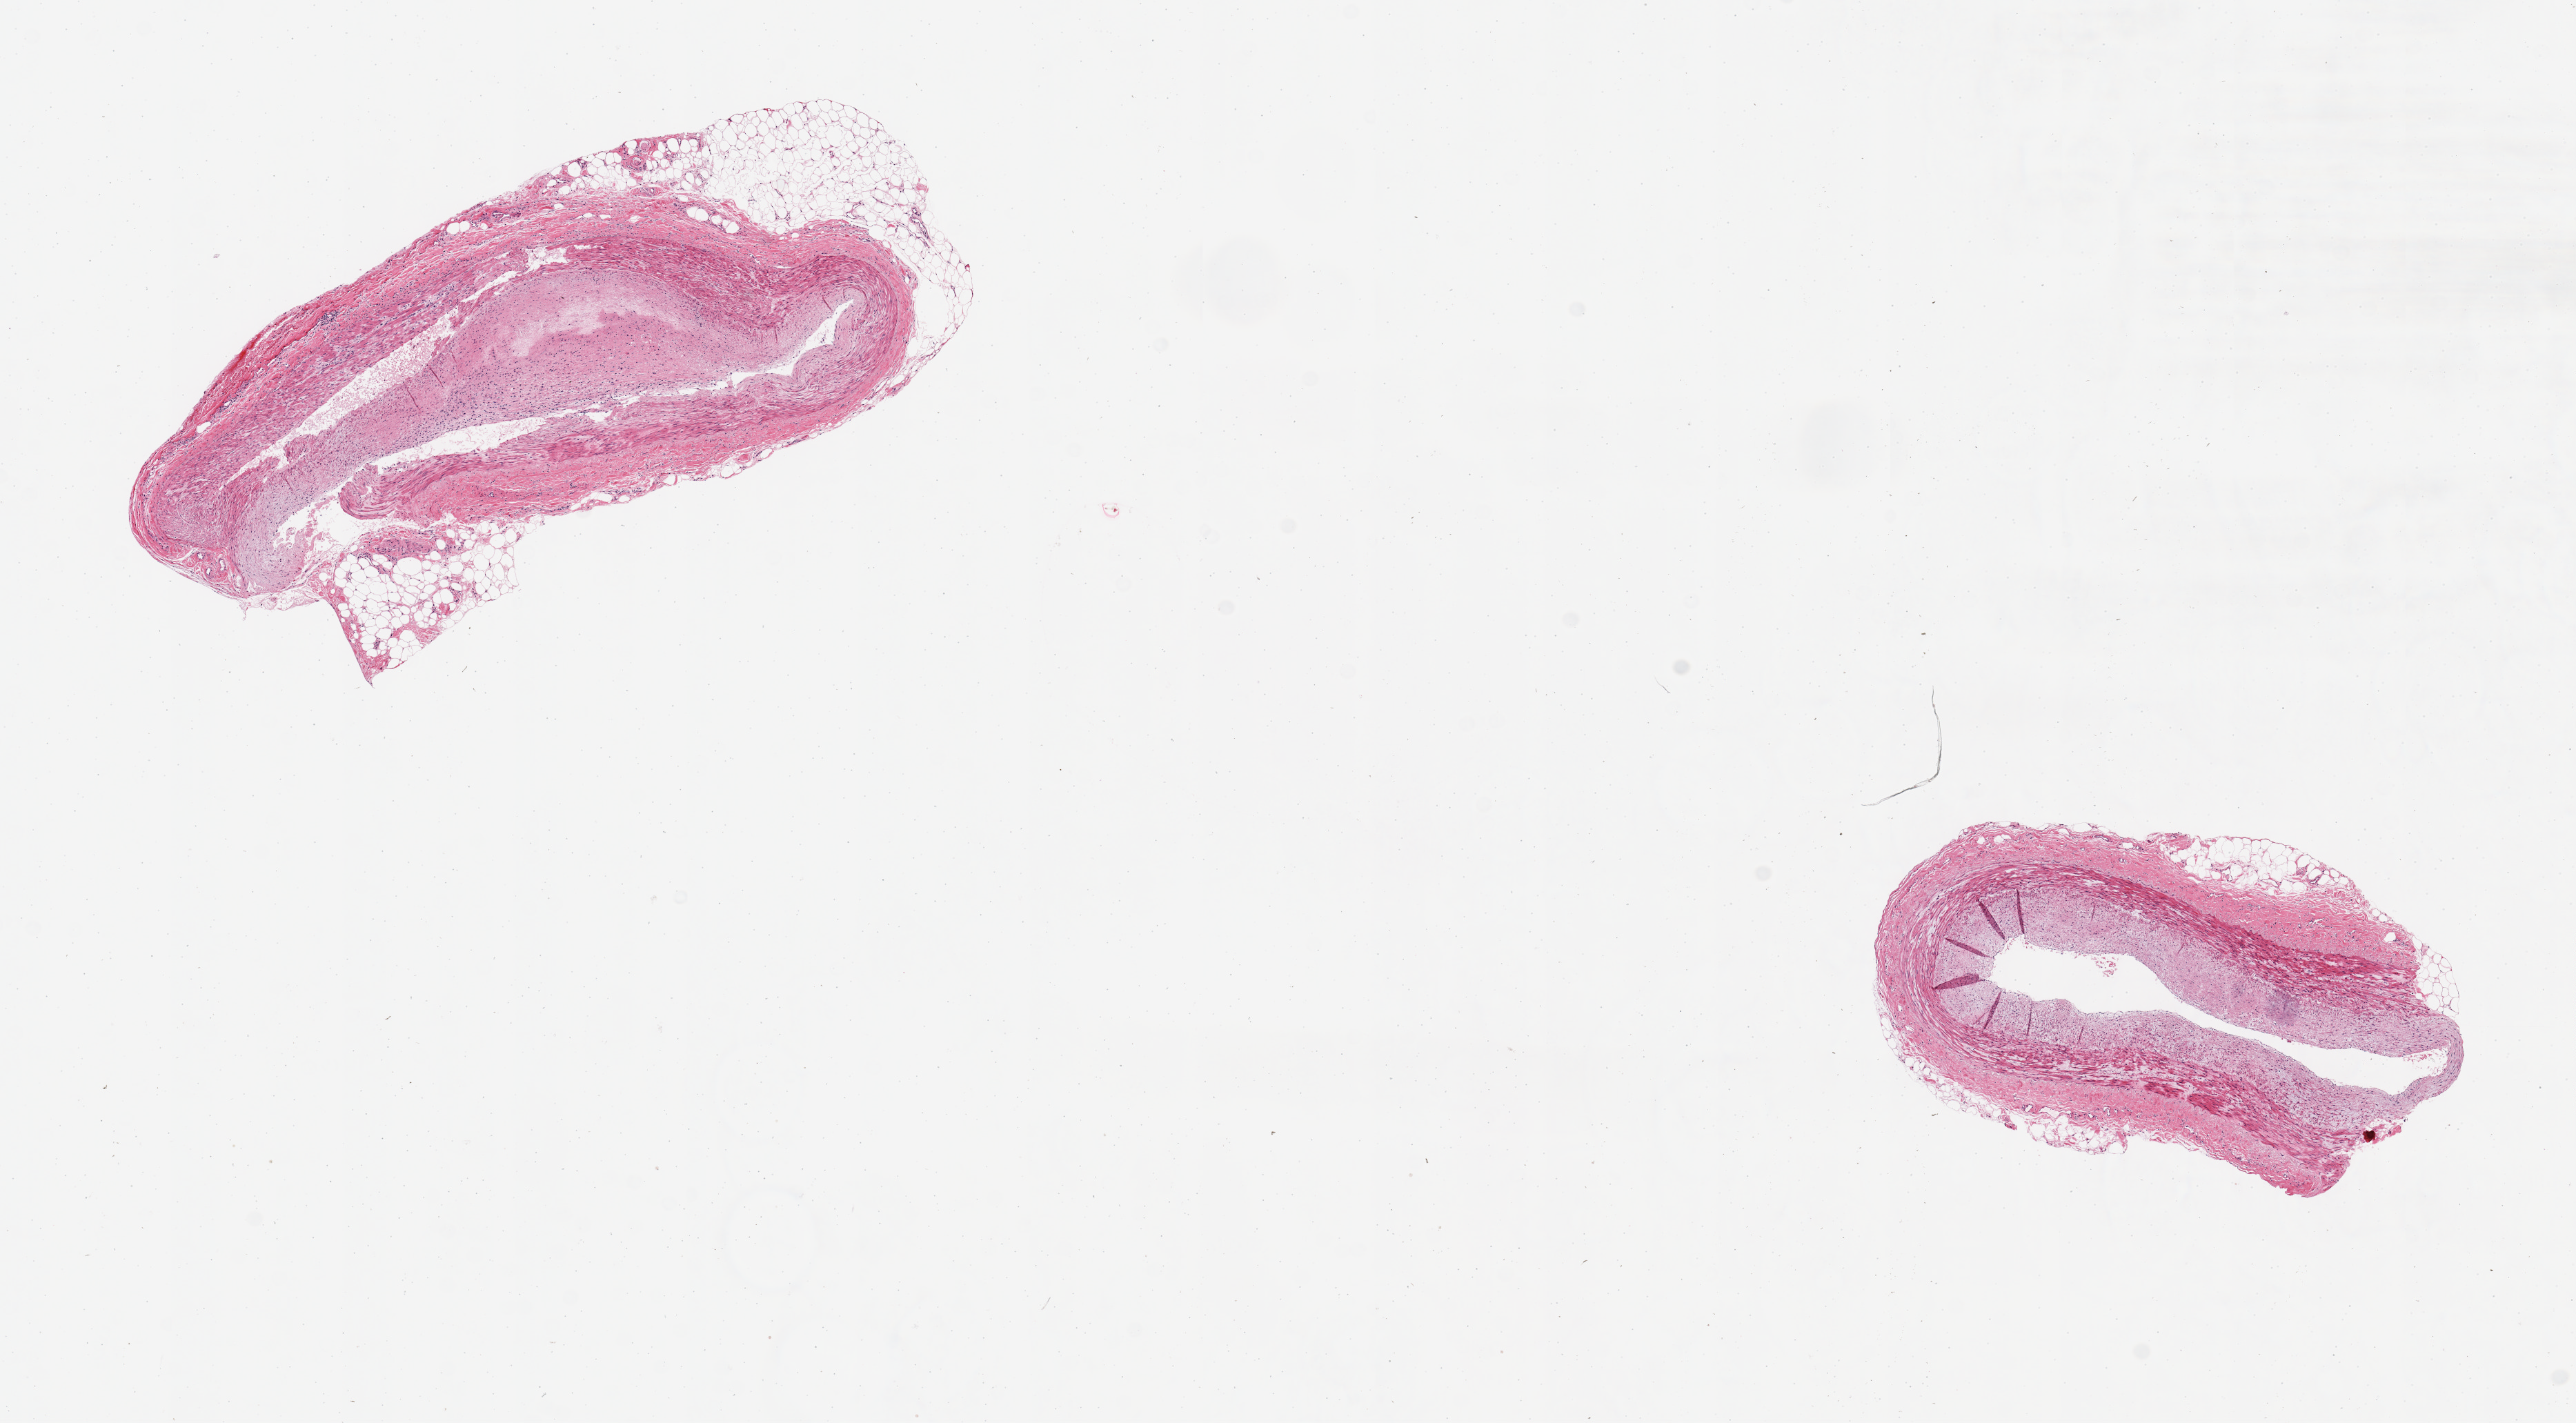
Hematoxylin and eosin (H&E) whole-slide image, a low-resolution overview of the entire scanned area, about 14.8 x 8.2 mm, PAXgene-fixed paraffin-embedded (PFPE) section, sampled site (target tissue): coronary artery, donor tissue sample. Donor sex: male.
Reviewer comment on this tissue sample: 2 pieces, subtotally occlusive atherosis.